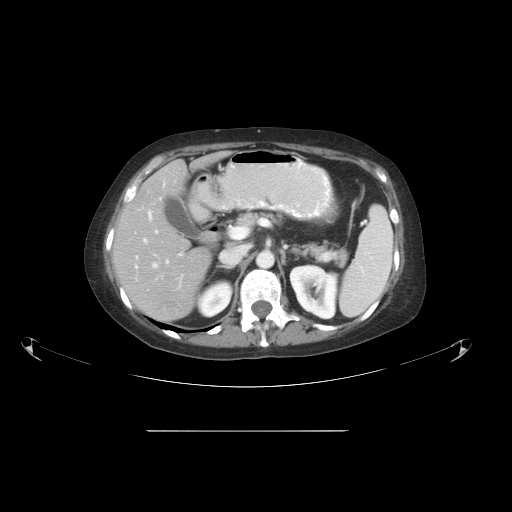
Contrast-enhanced abdominal CT, one axial slice; slice 31 of 51 in the series (ordered by position); reconstruction kernel STANDARD; 120 kVp; intravenous contrast given; soft-tissue window (W 400 / L 40 HU); 5 mm slice thickness; 512 × 512 image matrix, field of view 475 × 475 mm. Female patient, age 48 years. Case-level facts recorded for this patient, not image findings: diagnosis: colorectal cancer liver metastases, imaged before liver resection; multiple liver metastases: yes; largest metastasis: 1 cm; disease in both lobes: no.
Structures marked on this image (outlined manually by an expert reader):
- hepatic veins: box from (x=153, y=198) to (x=182, y=268) px
- liver: (x=114, y=161)–(x=213, y=322)
- planned liver remnant (the part of the liver to remain after resection): (x=114, y=161)–(x=213, y=322)
- portal vein (with intrahepatic branches): (x=135, y=211)–(x=183, y=277)